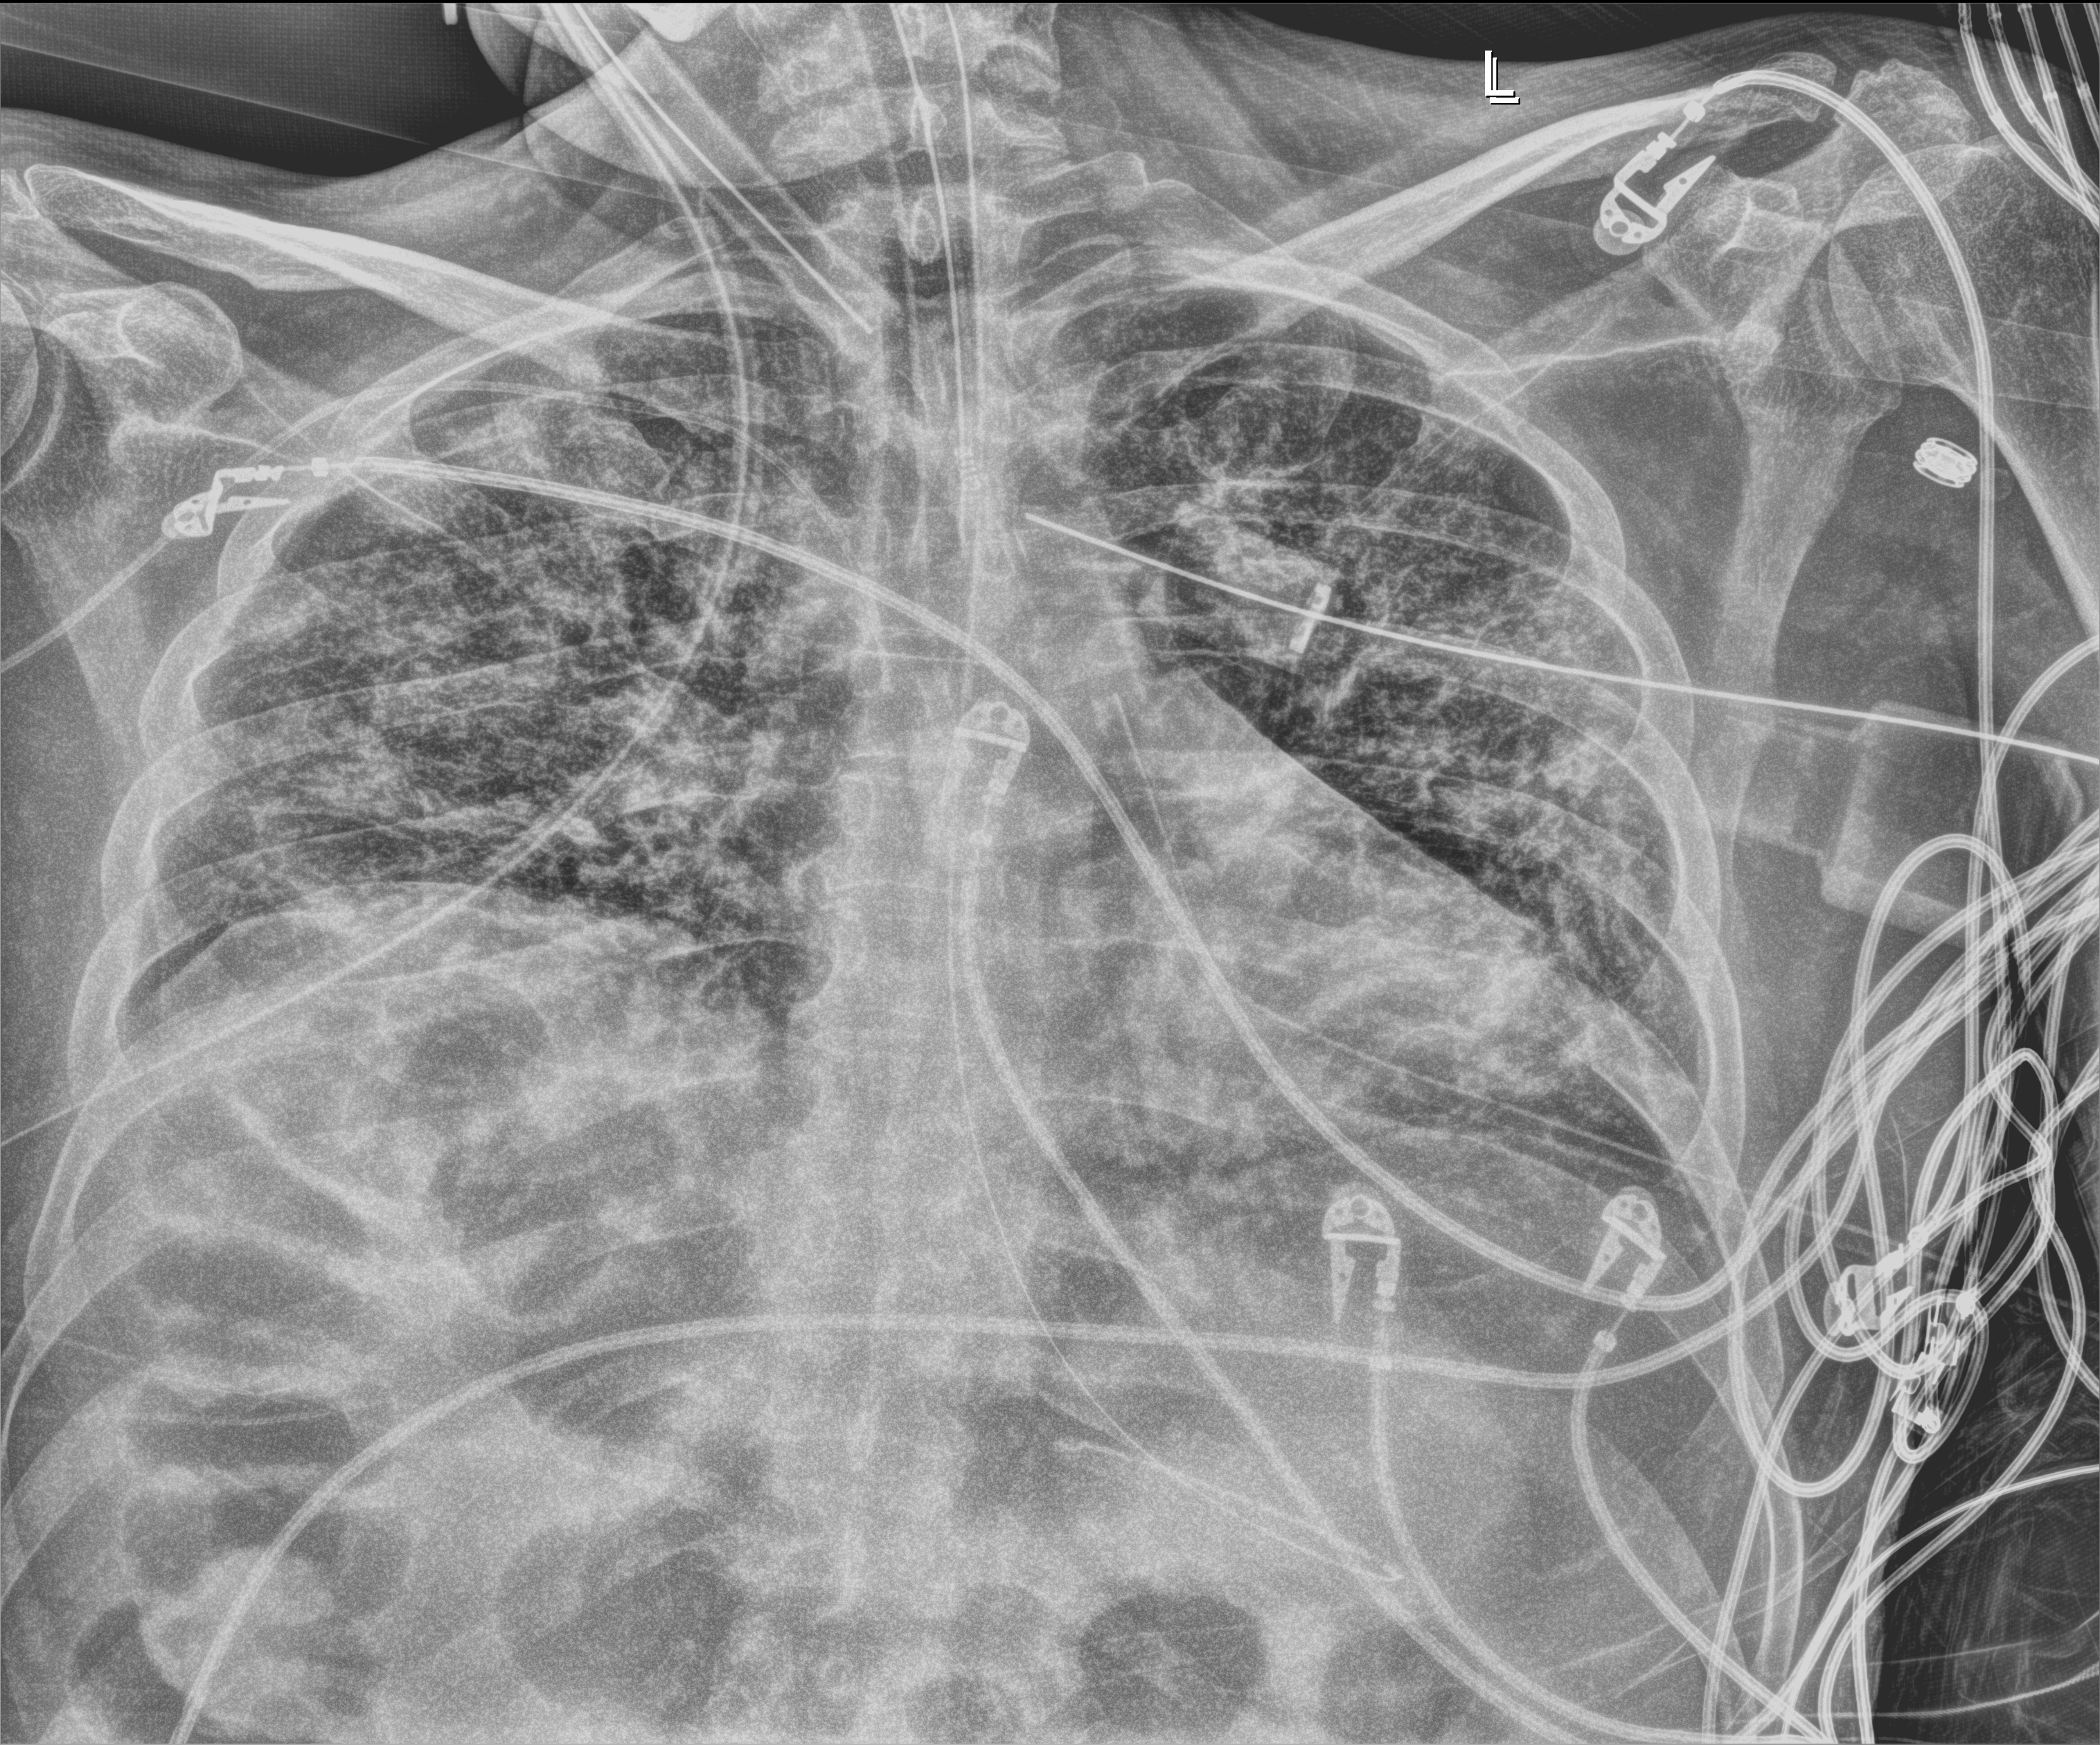
Portable chest radiograph; anteroposterior (AP) projection. Patient hospitalised with COVID-19; male, aged 18–59 years.
Admission-level facts for this patient (not findings on this image; timing relative to this image not recorded): mechanically ventilated during this hospital stay: yes.